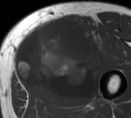
MRI of an extremity soft-tissue mass, one axial slice. Position 32 of 55 along the scan axis. MR volume resampled by the dataset authors to the PET/CT grid (not the native acquisition matrix). 3.27 mm slice thickness. 131 × 118 image matrix, field of view 128 × 115 mm. Male patient. Case-level facts recorded for this patient, not image findings: histological type: pleiomorphic liposarcoma; grade: high; site of the primary tumour: left thigh.
Structures marked on this image (expert contour drawn on MRI and transferred to this co-registered scan by the dataset authors):
- gross tumour volume including surrounding oedema: bounding box <14,17,108,102> (left, top, right, bottom; pixels)
- gross tumour volume (mass): <14,18,104,102>